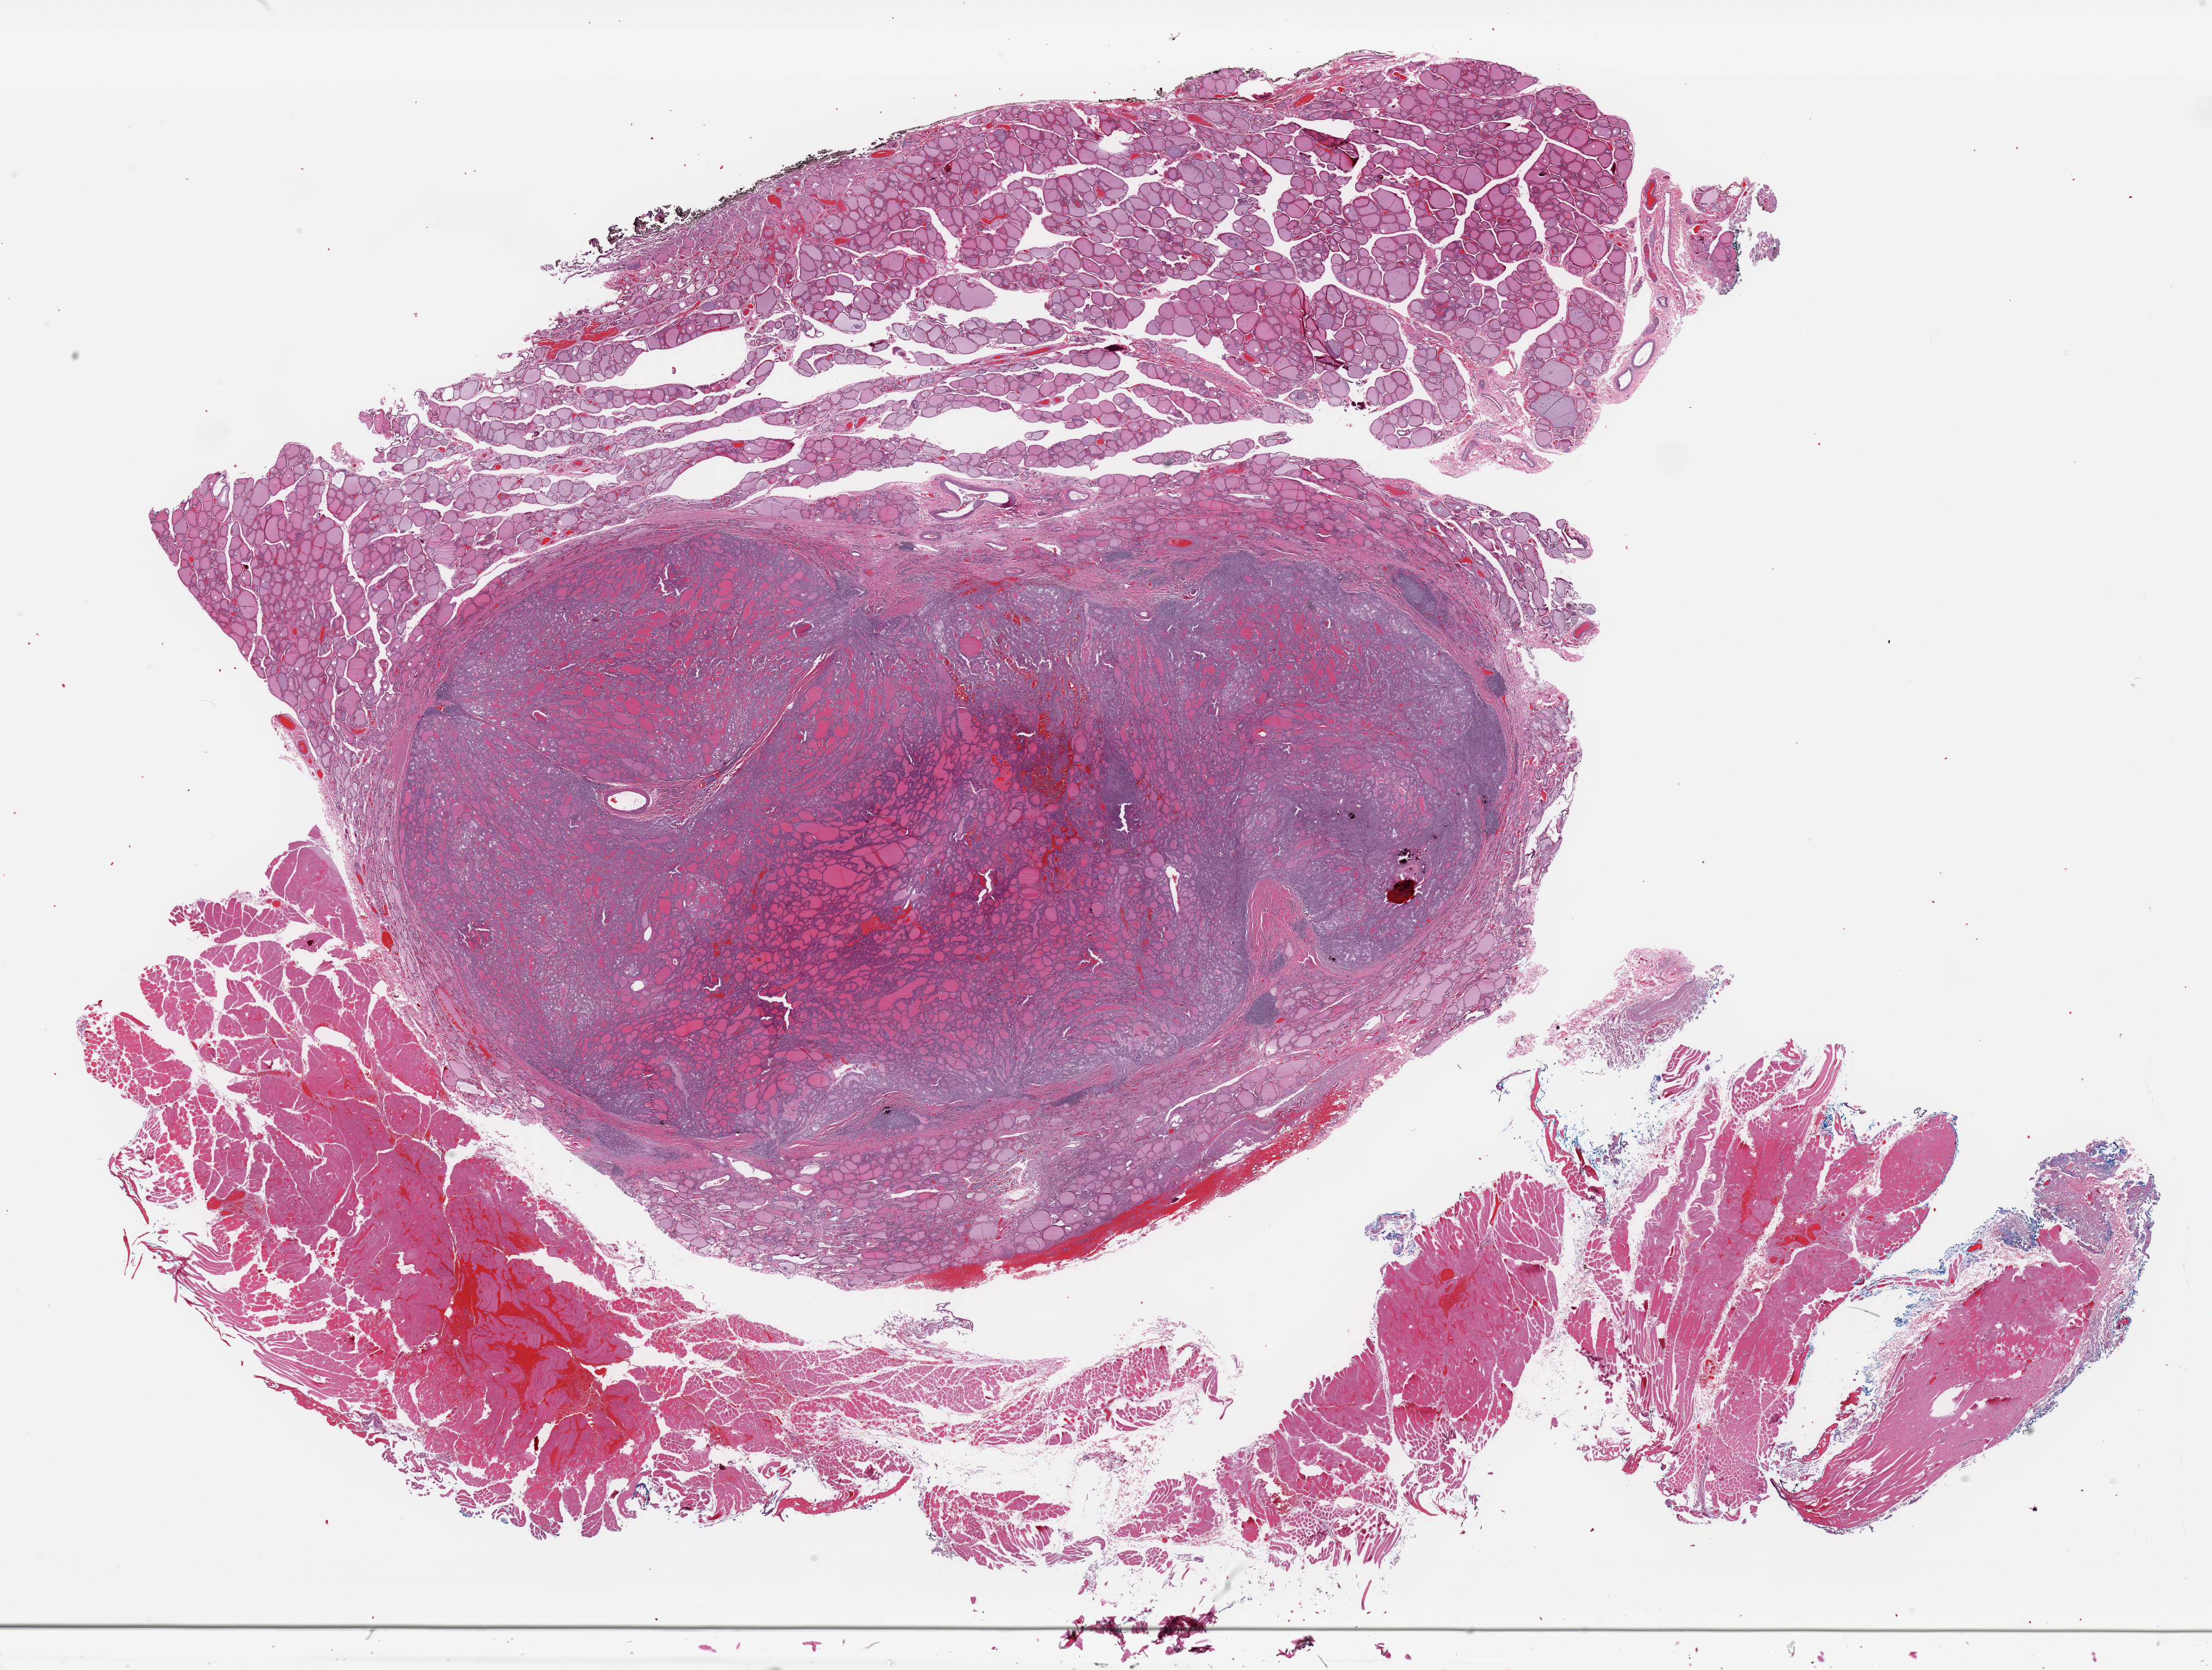
H&E-stained whole-slide image, whole scanned area (about 31.0 x 23.4 mm, from a 40x scan) shown as a low-resolution overview; formalin-fixed paraffin-embedded (FFPE) diagnostic section; primary tumour sample from the thyroid. Female, age 37 years at initial diagnosis.
• TNM: T1b N0 M0
• laterality: right
• histologic diagnosis: Papillary adenocarcinoma, NOS (thyroid gland)
• AJCC pathologic stage: I